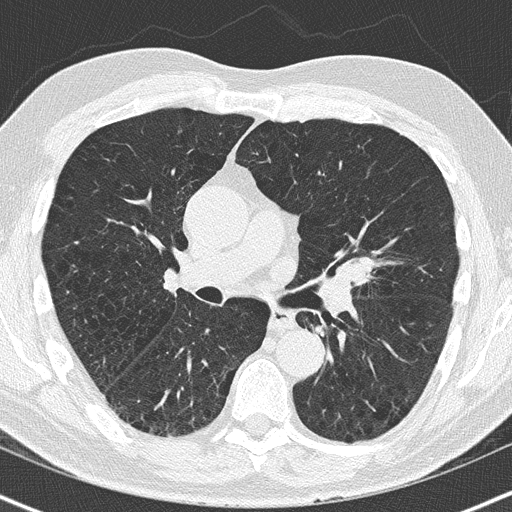
Low-dose screening chest CT, one axial slice. Position 90 of 163 along the scan axis. Reconstruction kernel B50f. Lung window (W 1500 / L -600 HU). 2 mm slice thickness. 512 × 512 image matrix, field of view 320 × 320 mm.
Outlined on this slice (manually delineated by an expert):
- lesion 1 (tumor, upper lobe of left lung): bounding box <336,256,376,284> (left, top, right, bottom; pixels)